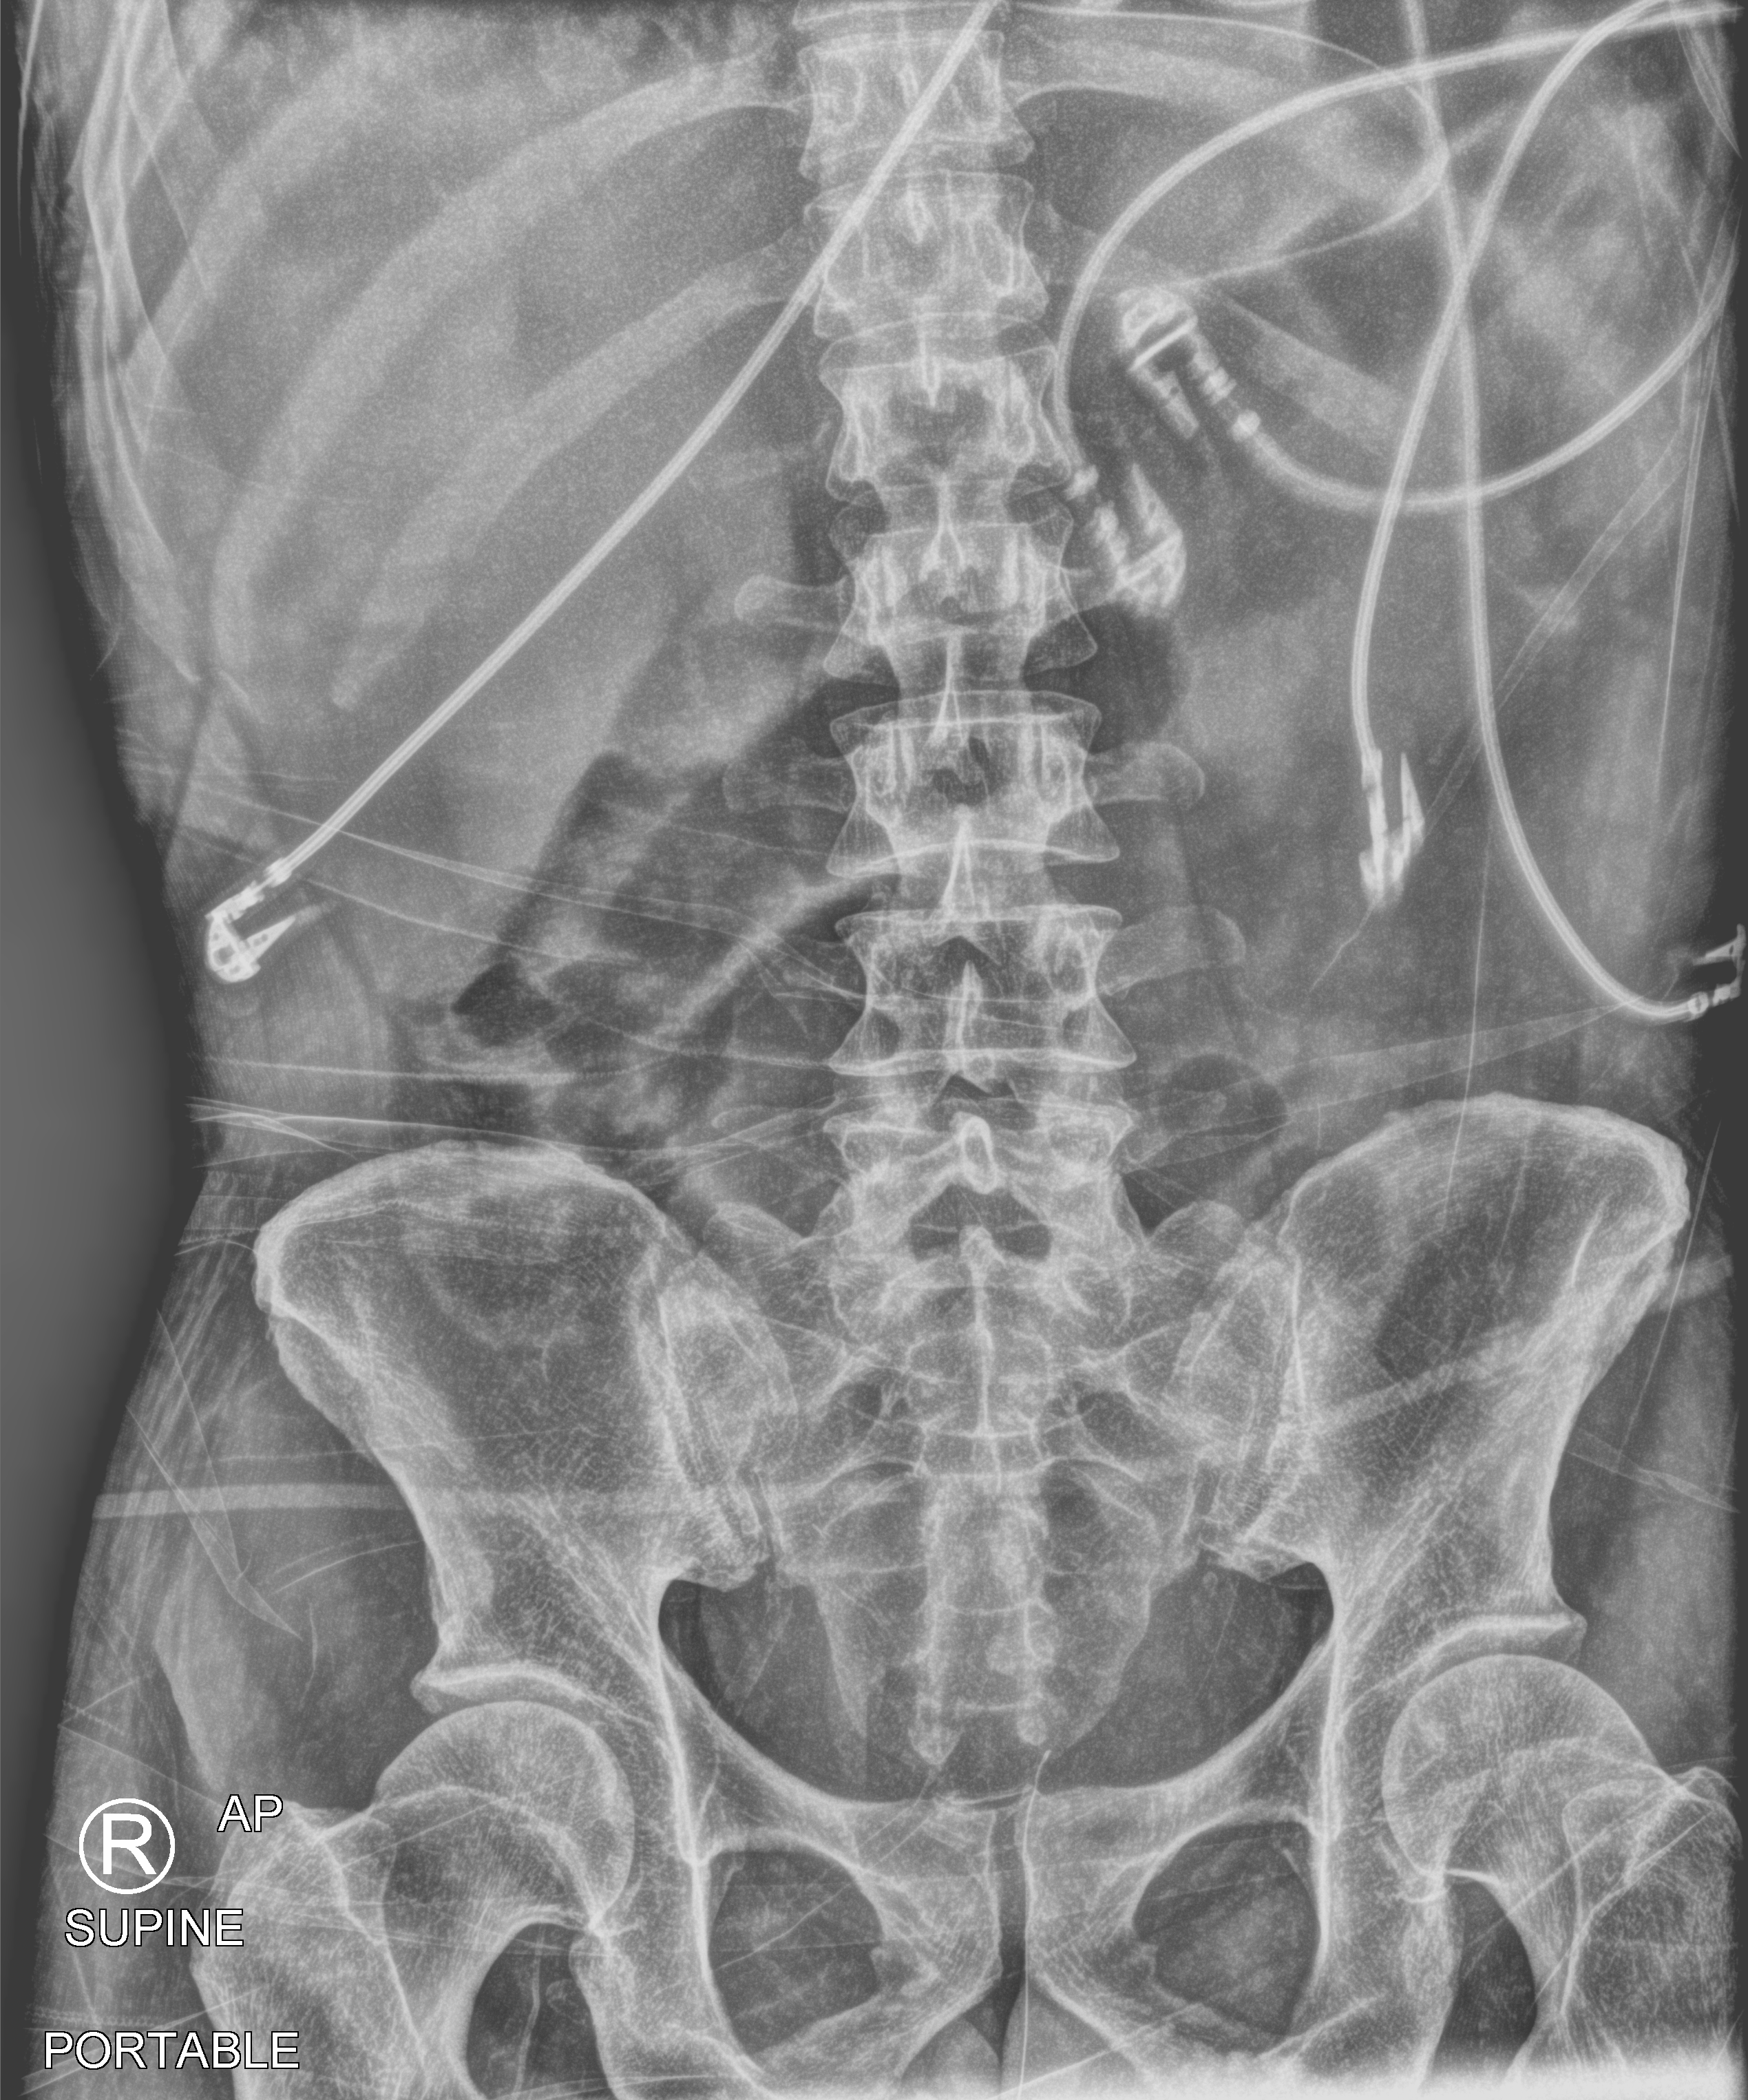
Abdomen X-ray (portable). Patient hospitalised with COVID-19; male, aged 18–59 years.
From the hospital-stay record, not from the radiograph (when in the stay this image was taken is not recorded):
- mechanically ventilated during this hospital stay: yes
- admitted to intensive care during this hospital stay: yes